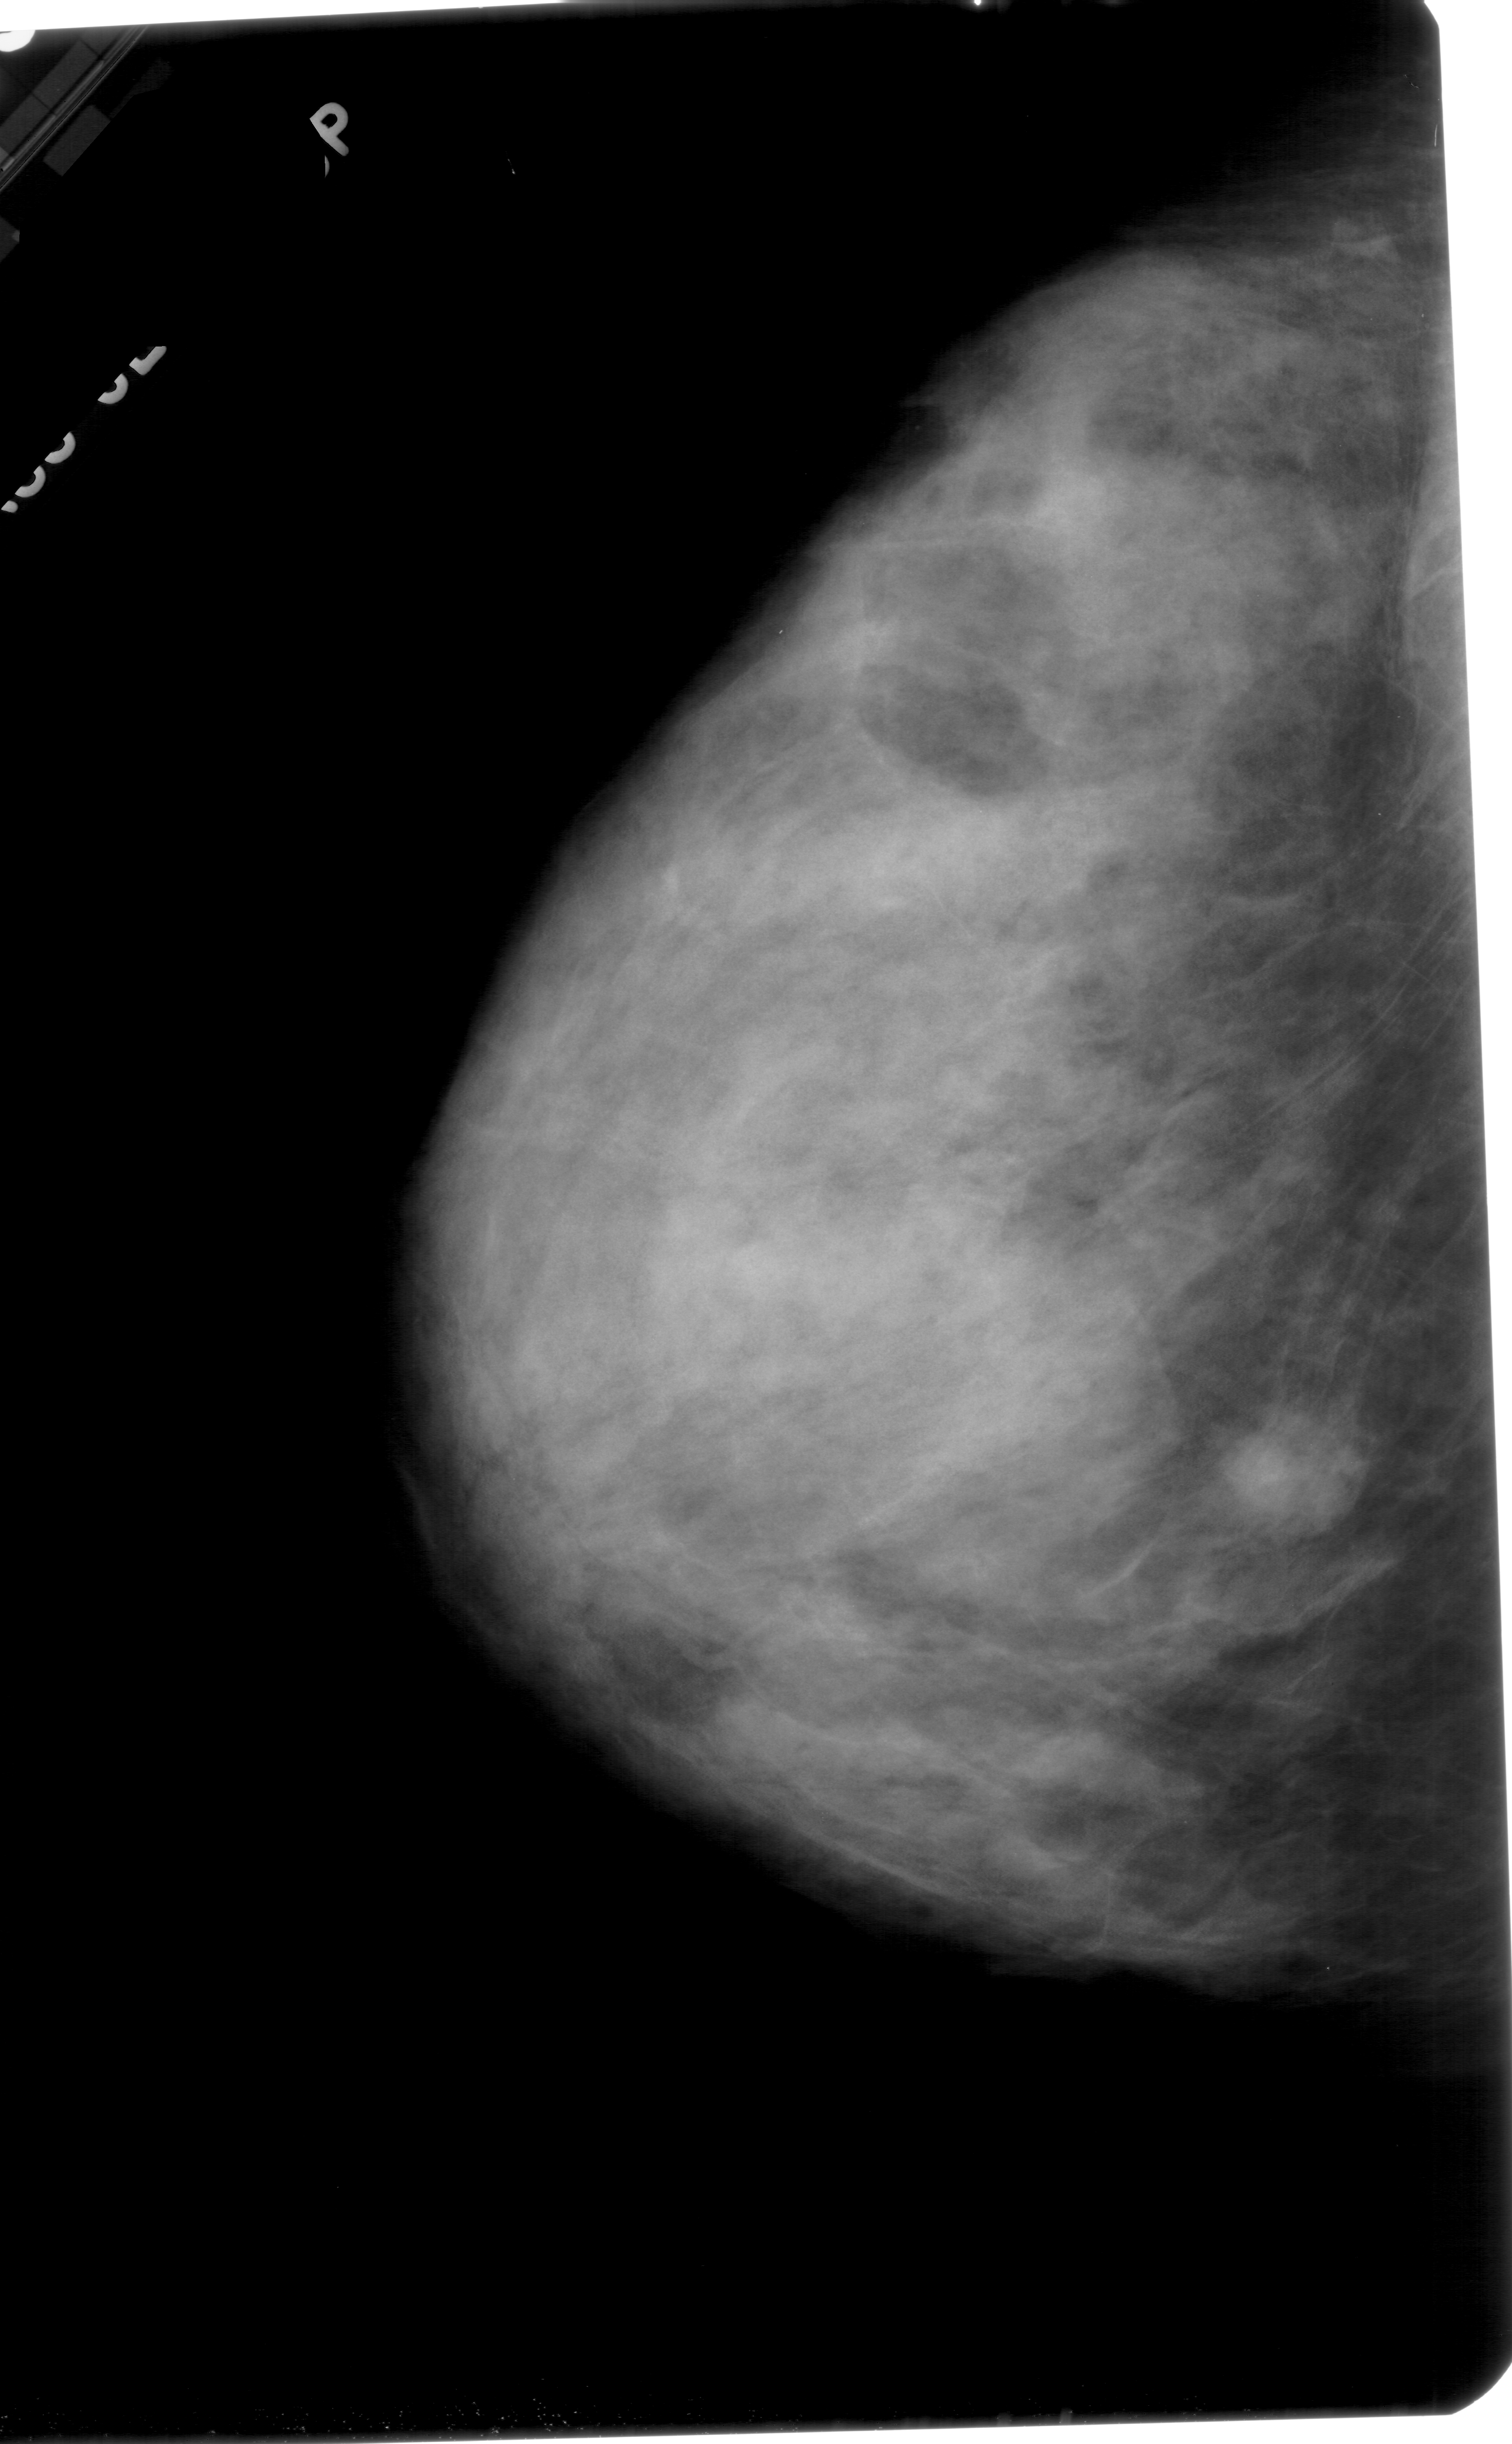
Scanned film-screen mammogram, left breast, CC view, BI-RADS breast density category 4 (scale 1–4).
Mass, shape round, margins ill defined; BI-RADS assessment category 4; subtlety rating 3 on a 1 (subtle) to 5 (obvious) scale; pathology (as recorded): malignant.